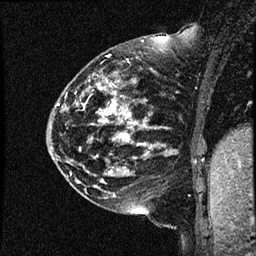
Breast MRI (dynamic contrast-enhanced), one sagittal slice. Slice 15 of 44 in the series (ordered by position). Dynamic contrast-enhanced study with each time point stored as its own series, time point 2 of 4 at this slice position (early post-contrast, ordered by acquisition time). 1.5 T. TE 4.2 ms, TR 17.7 ms. 256 × 256 image matrix. Patient: female, 52 years. Case-level facts recorded for this patient, not image findings: setting: breast cancer imaged before/during neoadjuvant chemotherapy; receptor status: HR-positive, HER2-negative.
Outlined on this slice (semi-automatic segmentation, software-assisted and operator-edited):
- analysis volume of interest (the breast-tissue region the enhancement analysis was run in; not a lesion): bounding box (x1, y1, x2, y2) in pixels: (47, 48, 163, 147)
- tumour enhancement mask (voxels above the 100 % enhancement threshold inside the analysis volume of interest): (99, 79, 134, 140)